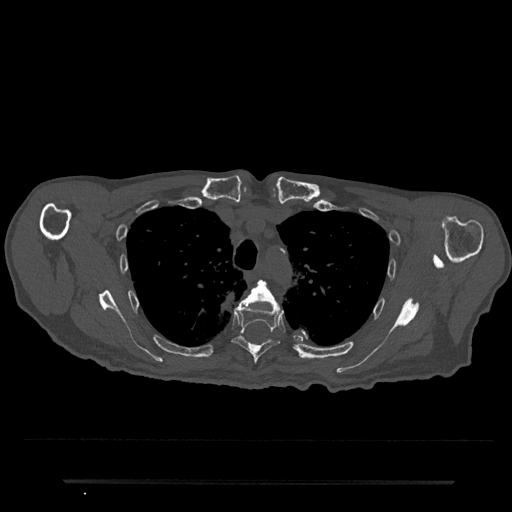
CT including the spine, one axial slice. Position 585 of 797 along the scan axis. Bone window (W 1800 / L 400 HU). 0.5 mm slice thickness. 512 × 512 image matrix, field of view 427 × 427 mm. Patient: male, 74 years. From the clinical record (not read from this slice): primary cancer: prostate.
Outlined on this slice (semi-automatically segmented with operator editing):
- T4 vertebra: bounding box <245,280,277,305> (left, top, right, bottom; pixels)
- T5 vertebra: <232,299,282,364>